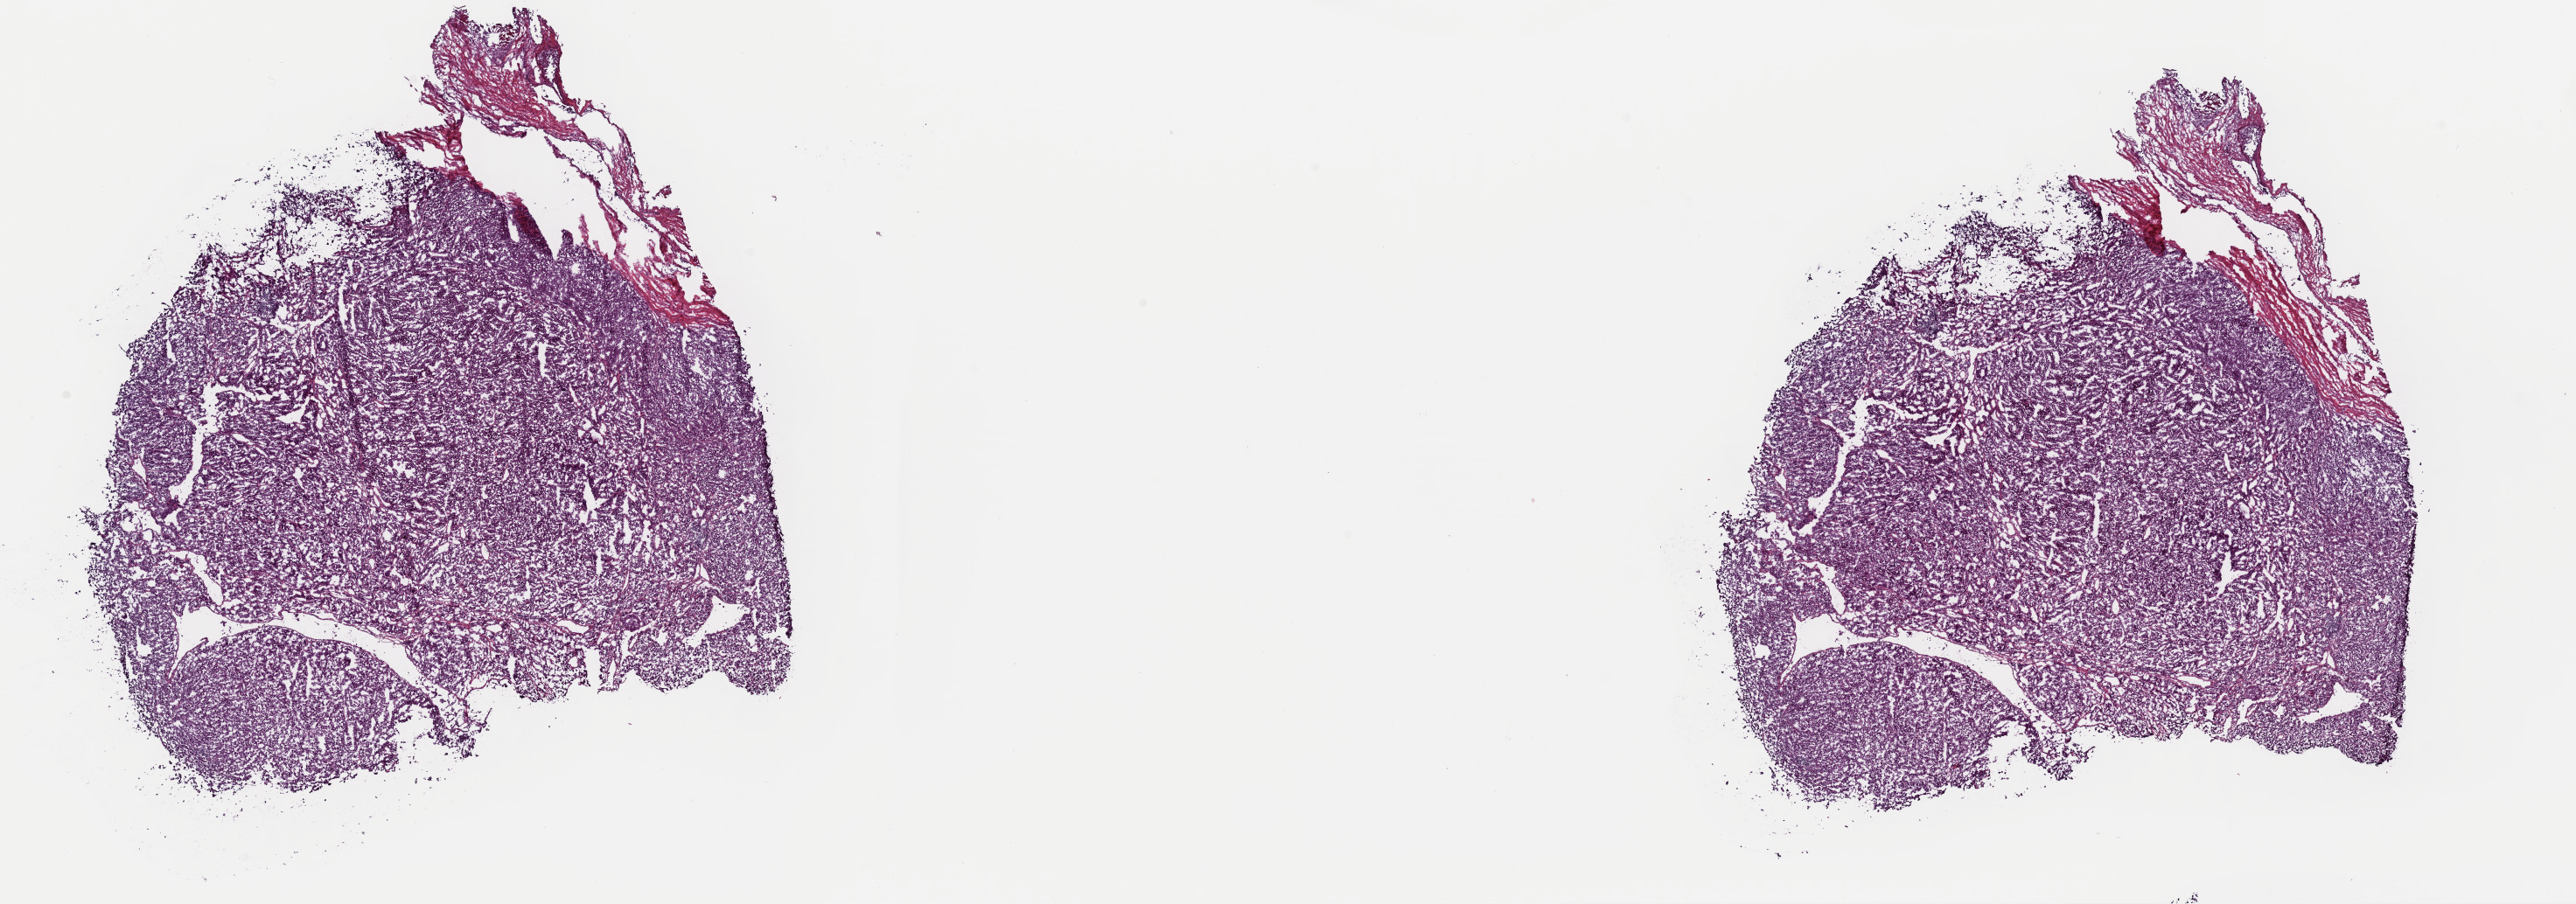
Digitized Hematoxylin and eosin (H&E) stained tissue section (whole slide), whole scanned area (about 23.3 x 8.2 mm, from a 40x scan) shown as a low-resolution overview, frozen section from the top of the tissue portion, adrenal cortex, primary tumour sample. Male, age 49 years at initial diagnosis. Pathologist review of this section (percent, as recorded): tumour cells 99%, tumour nuclei 99%, normal cells 0%, stromal cells 1%, necrosis 0%. Inflammatory infiltration, as recorded: lymphocyte infiltration 0%, monocyte infiltration 0%, neutrophil infiltration 0%.
• laterality: left
• diagnosis: Adrenal cortical carcinoma